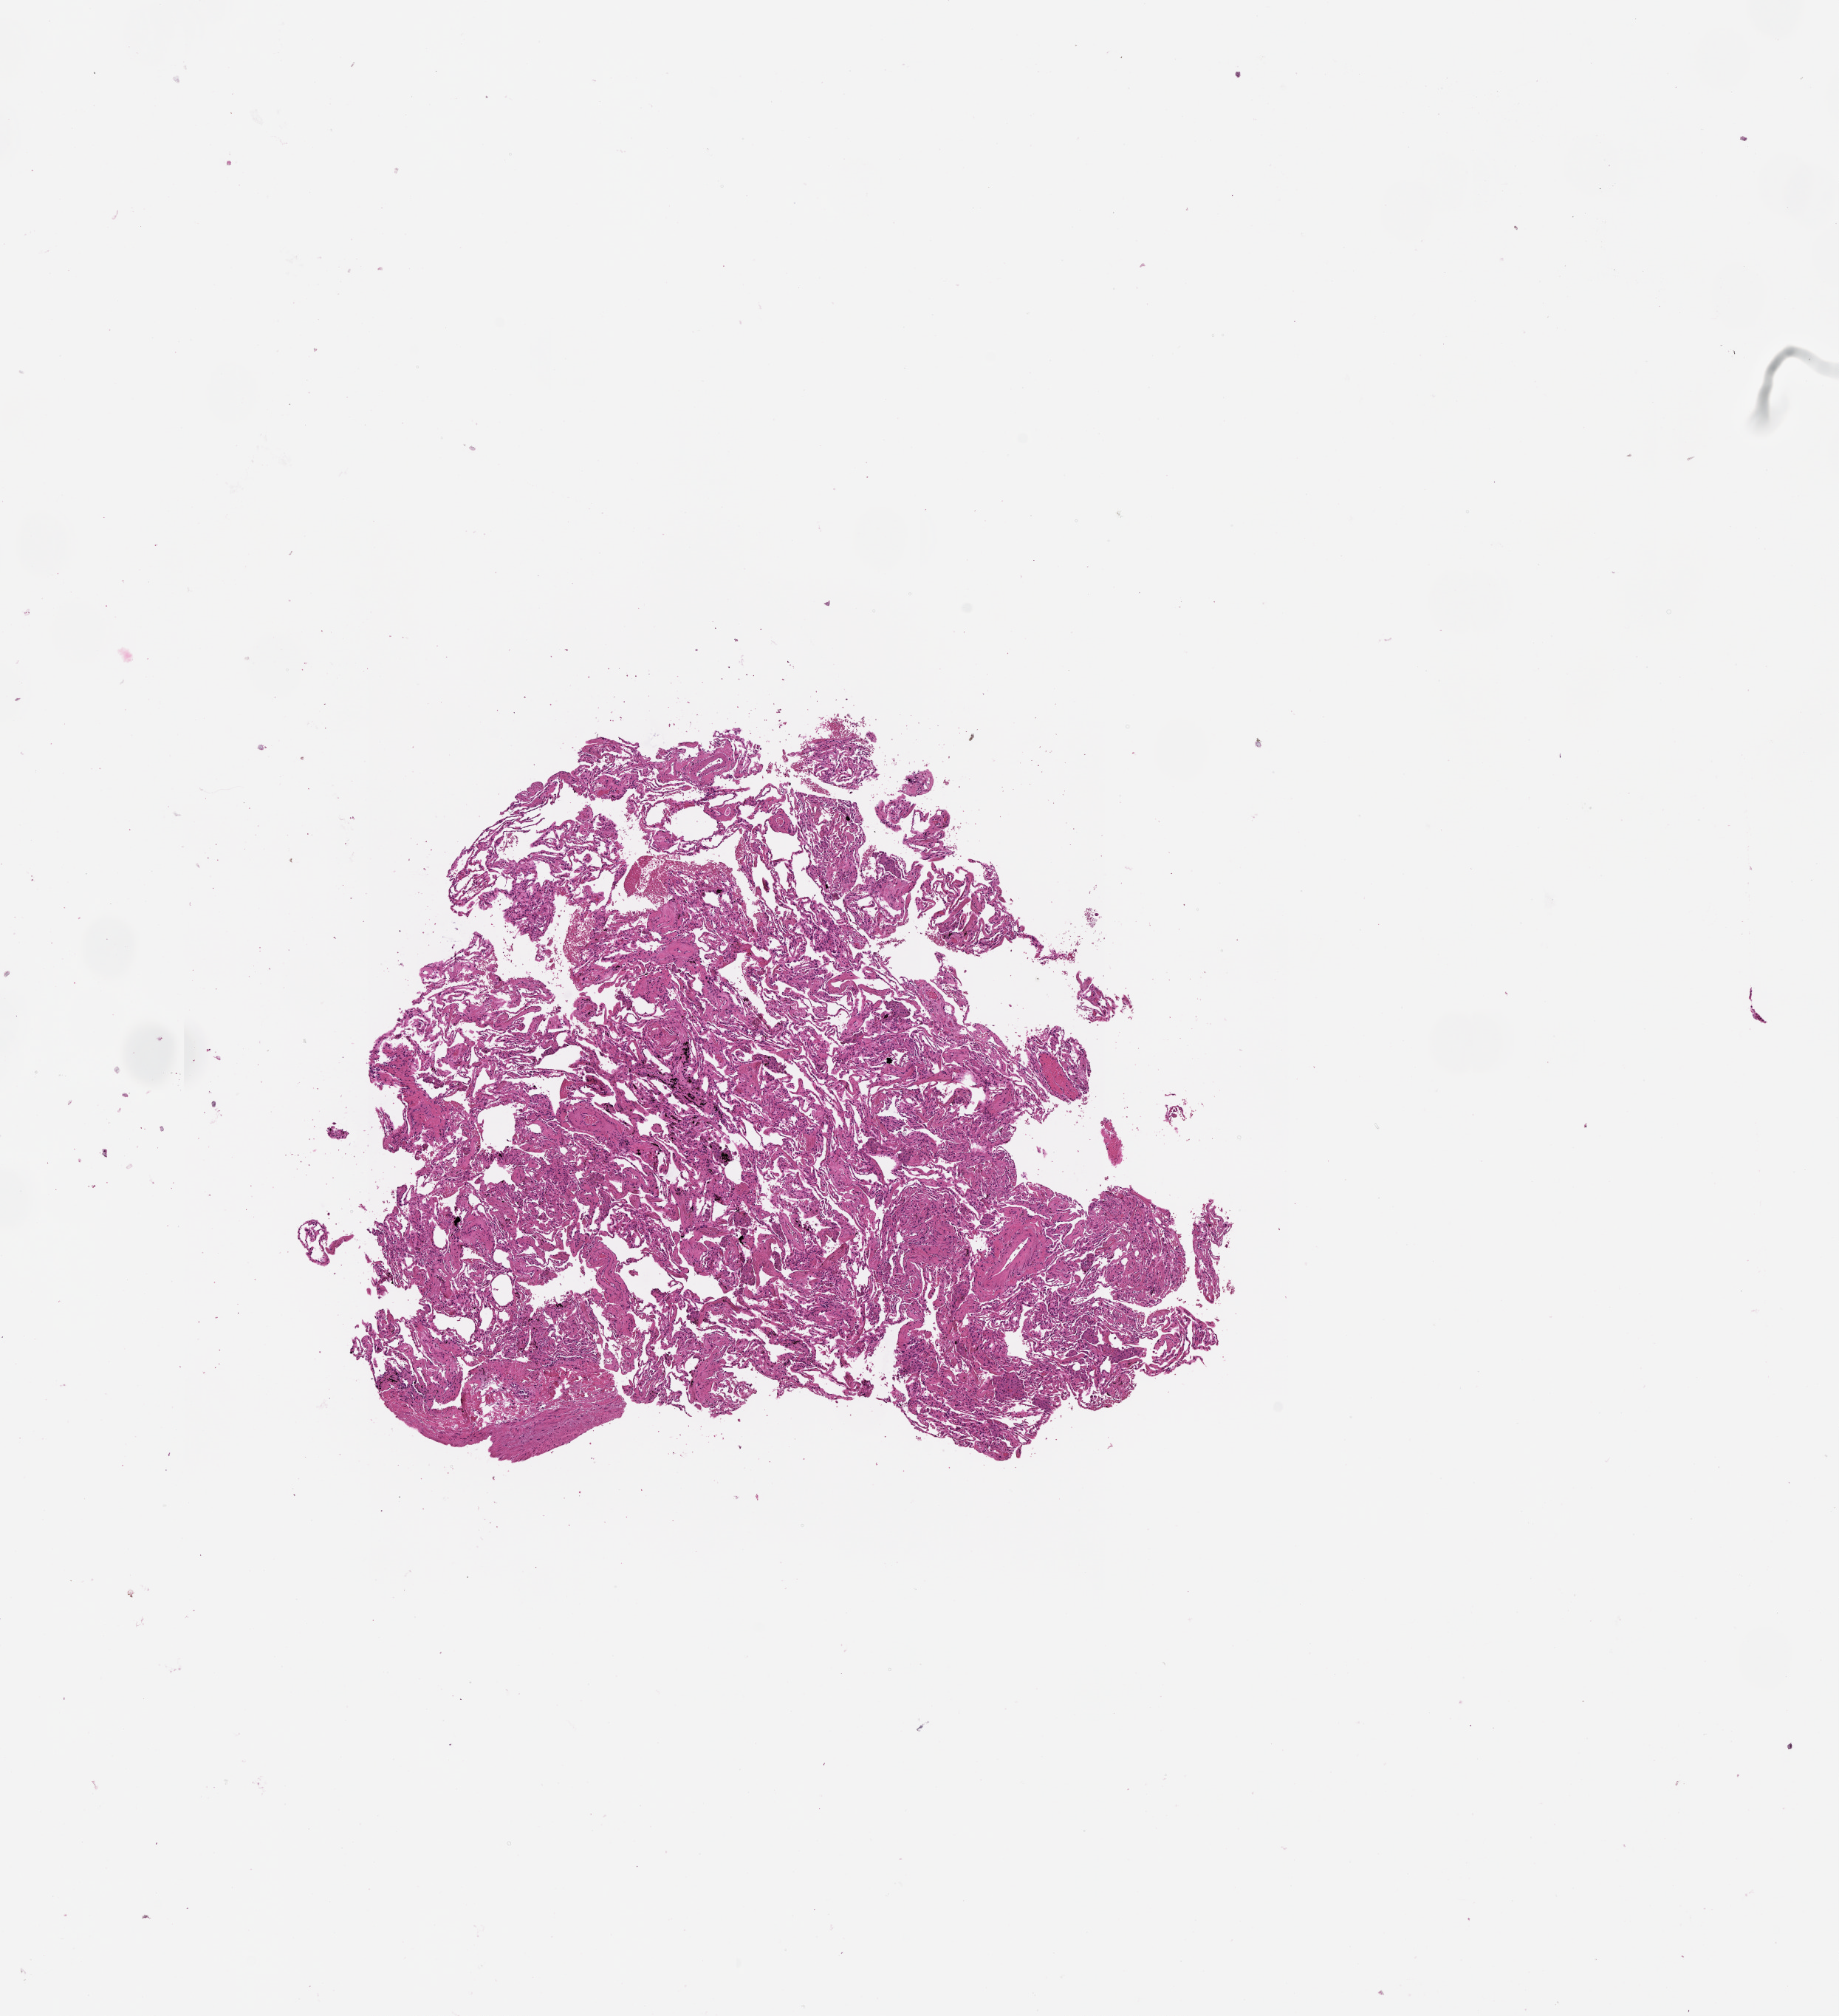
Hematoxylin and eosin (H&E) stained whole-slide image, shown as a low-resolution overview of the whole scanned area (about 10.0 x 11.0 mm, acquisition: 20x scan), lung, tissue type not recorded.
* patient diagnosis (cohort enrolment): squamous cell carcinoma (lung)